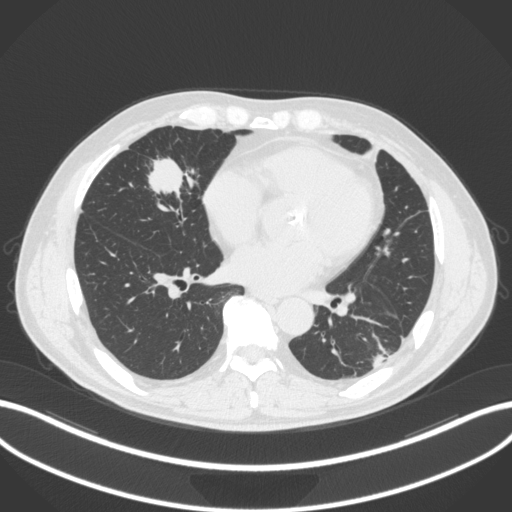
Chest CT, one axial slice; slice 116 of 399 in the series (ordered by position); lung window (W 1500 / L -600 HU); 512 × 512 image matrix. Patient: male, 59 years. Case-level facts recorded for this patient, not image findings: clinical TNM (as recorded): T2a N1 M0.
Annotated regions visible in this slice (bounding box drawn by a radiologist):
- lung tumour (recorded histology: adenocarcinoma): box from (x=139, y=153) to (x=201, y=209) px